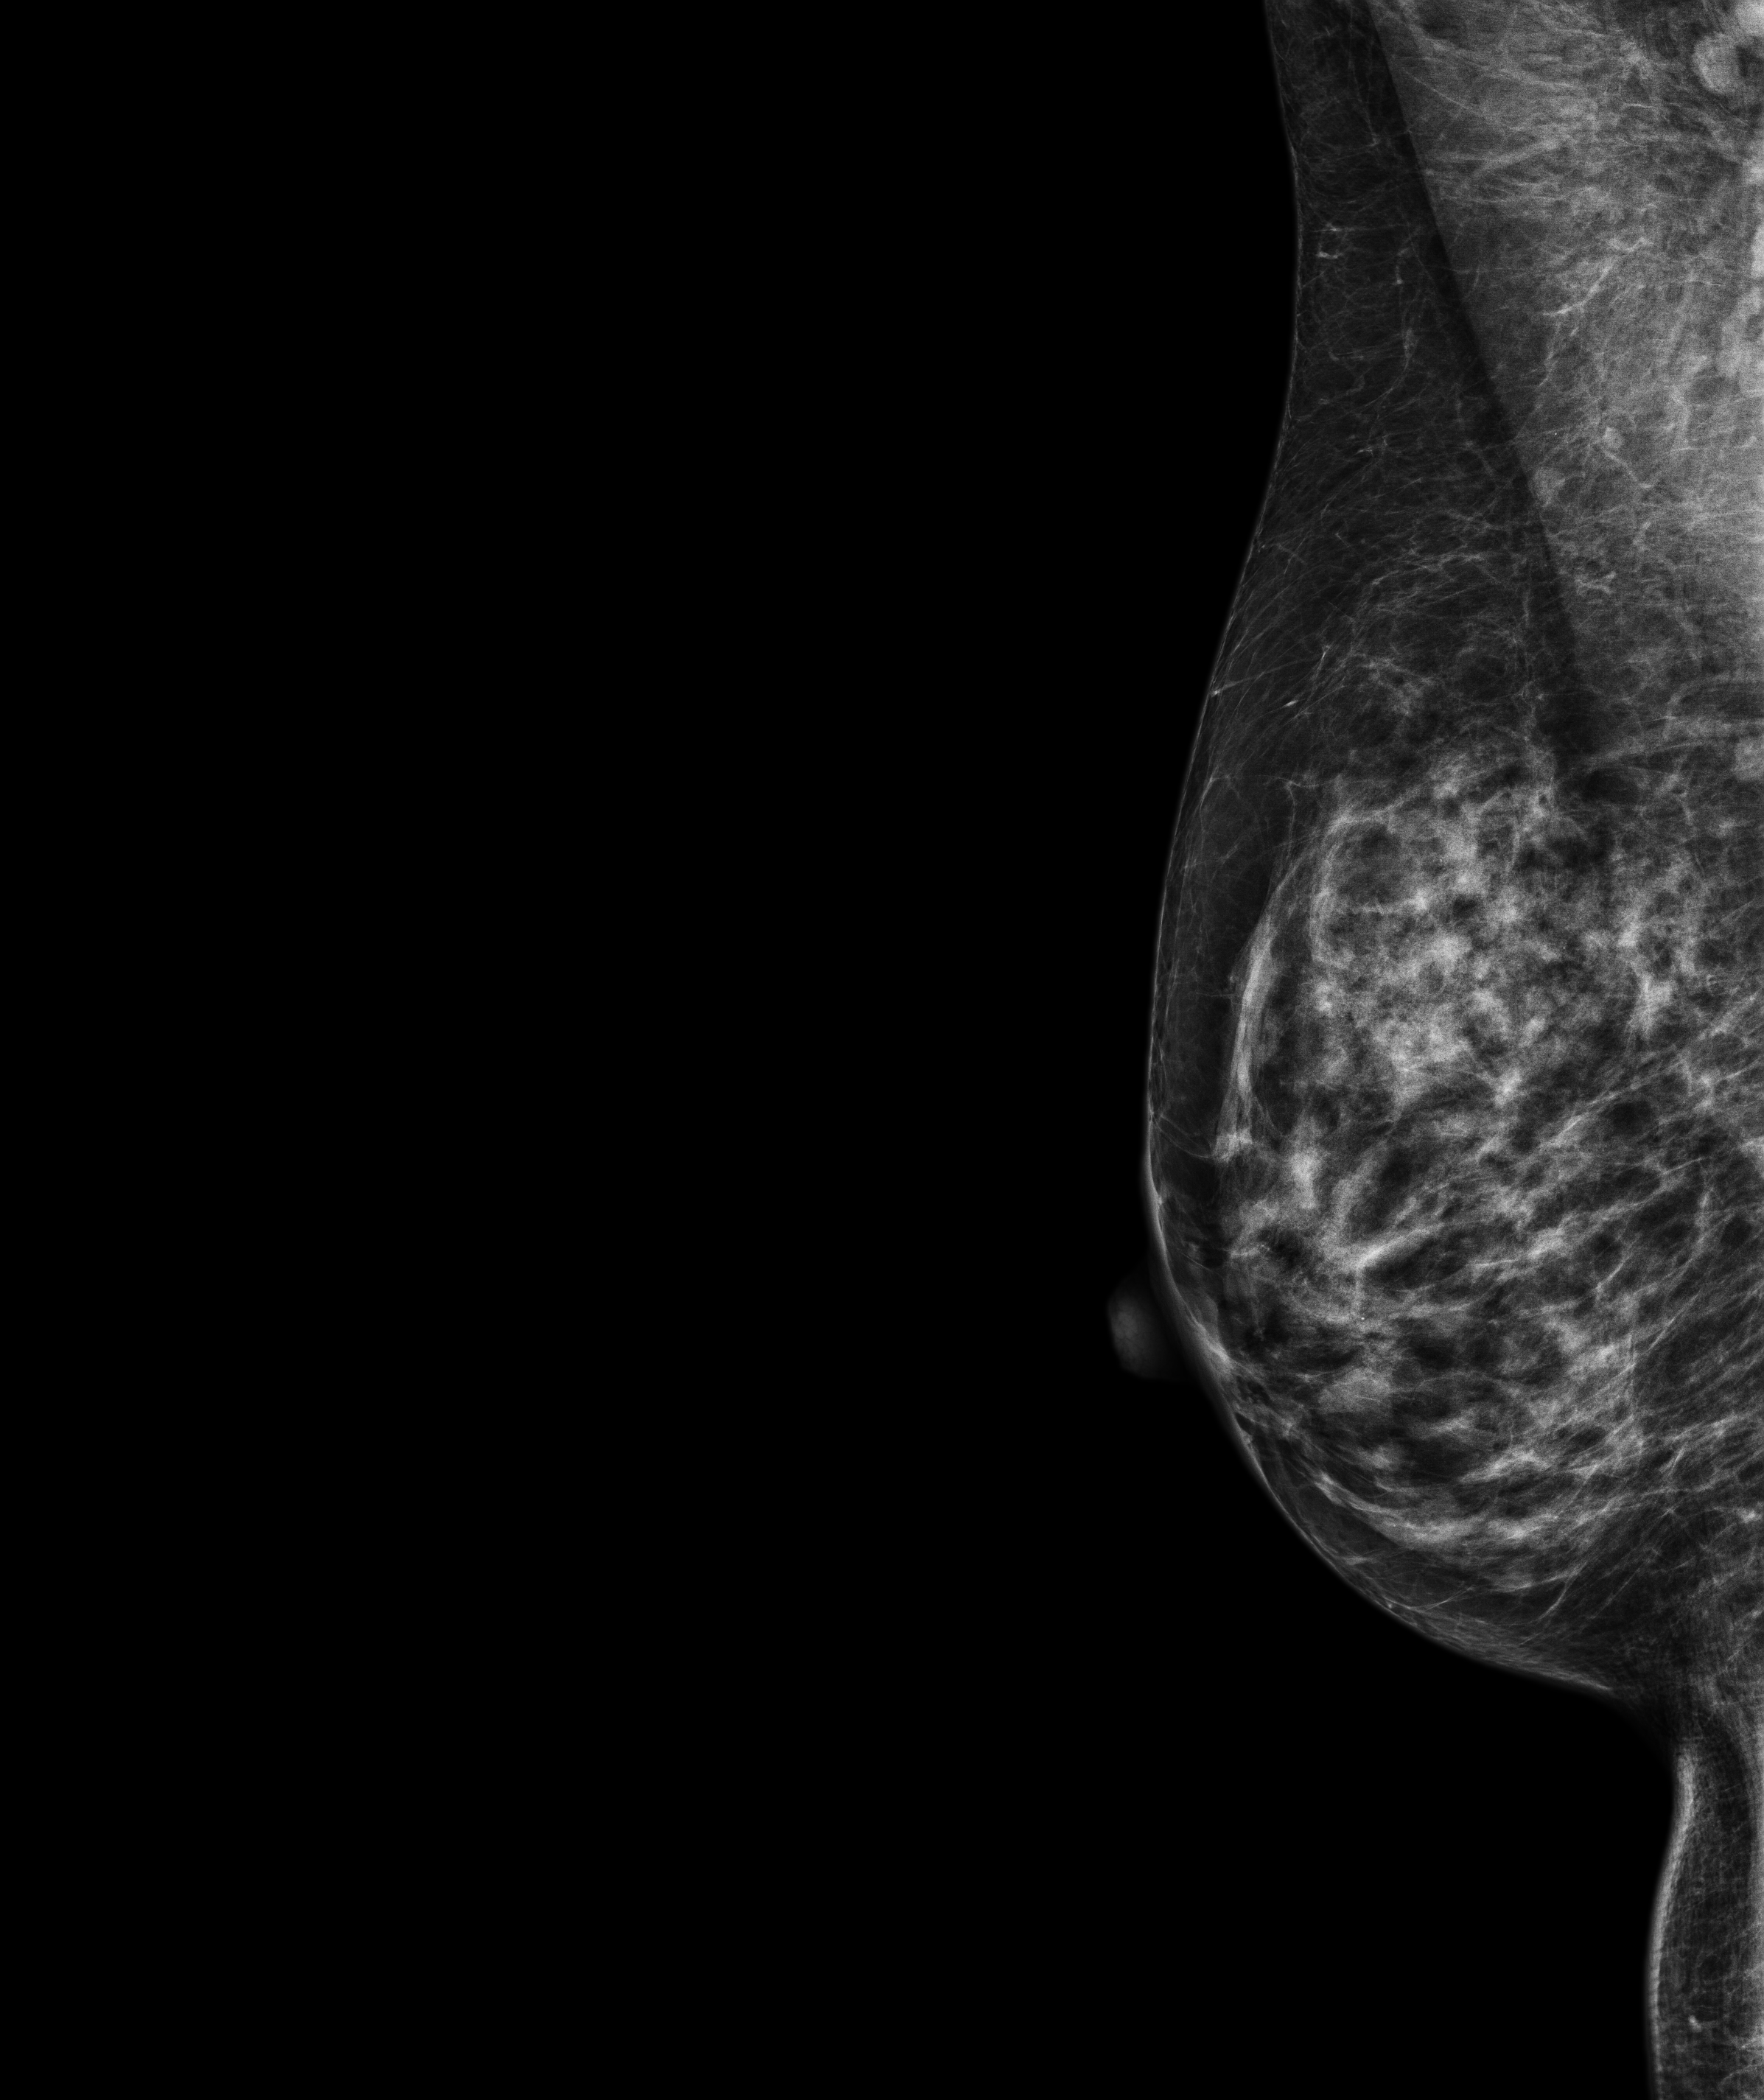
Screening examination. Patient: female, 59 years.
Image type: full-field digital mammogram. Breast: right. Projection: mediolateral oblique (MLO) view.